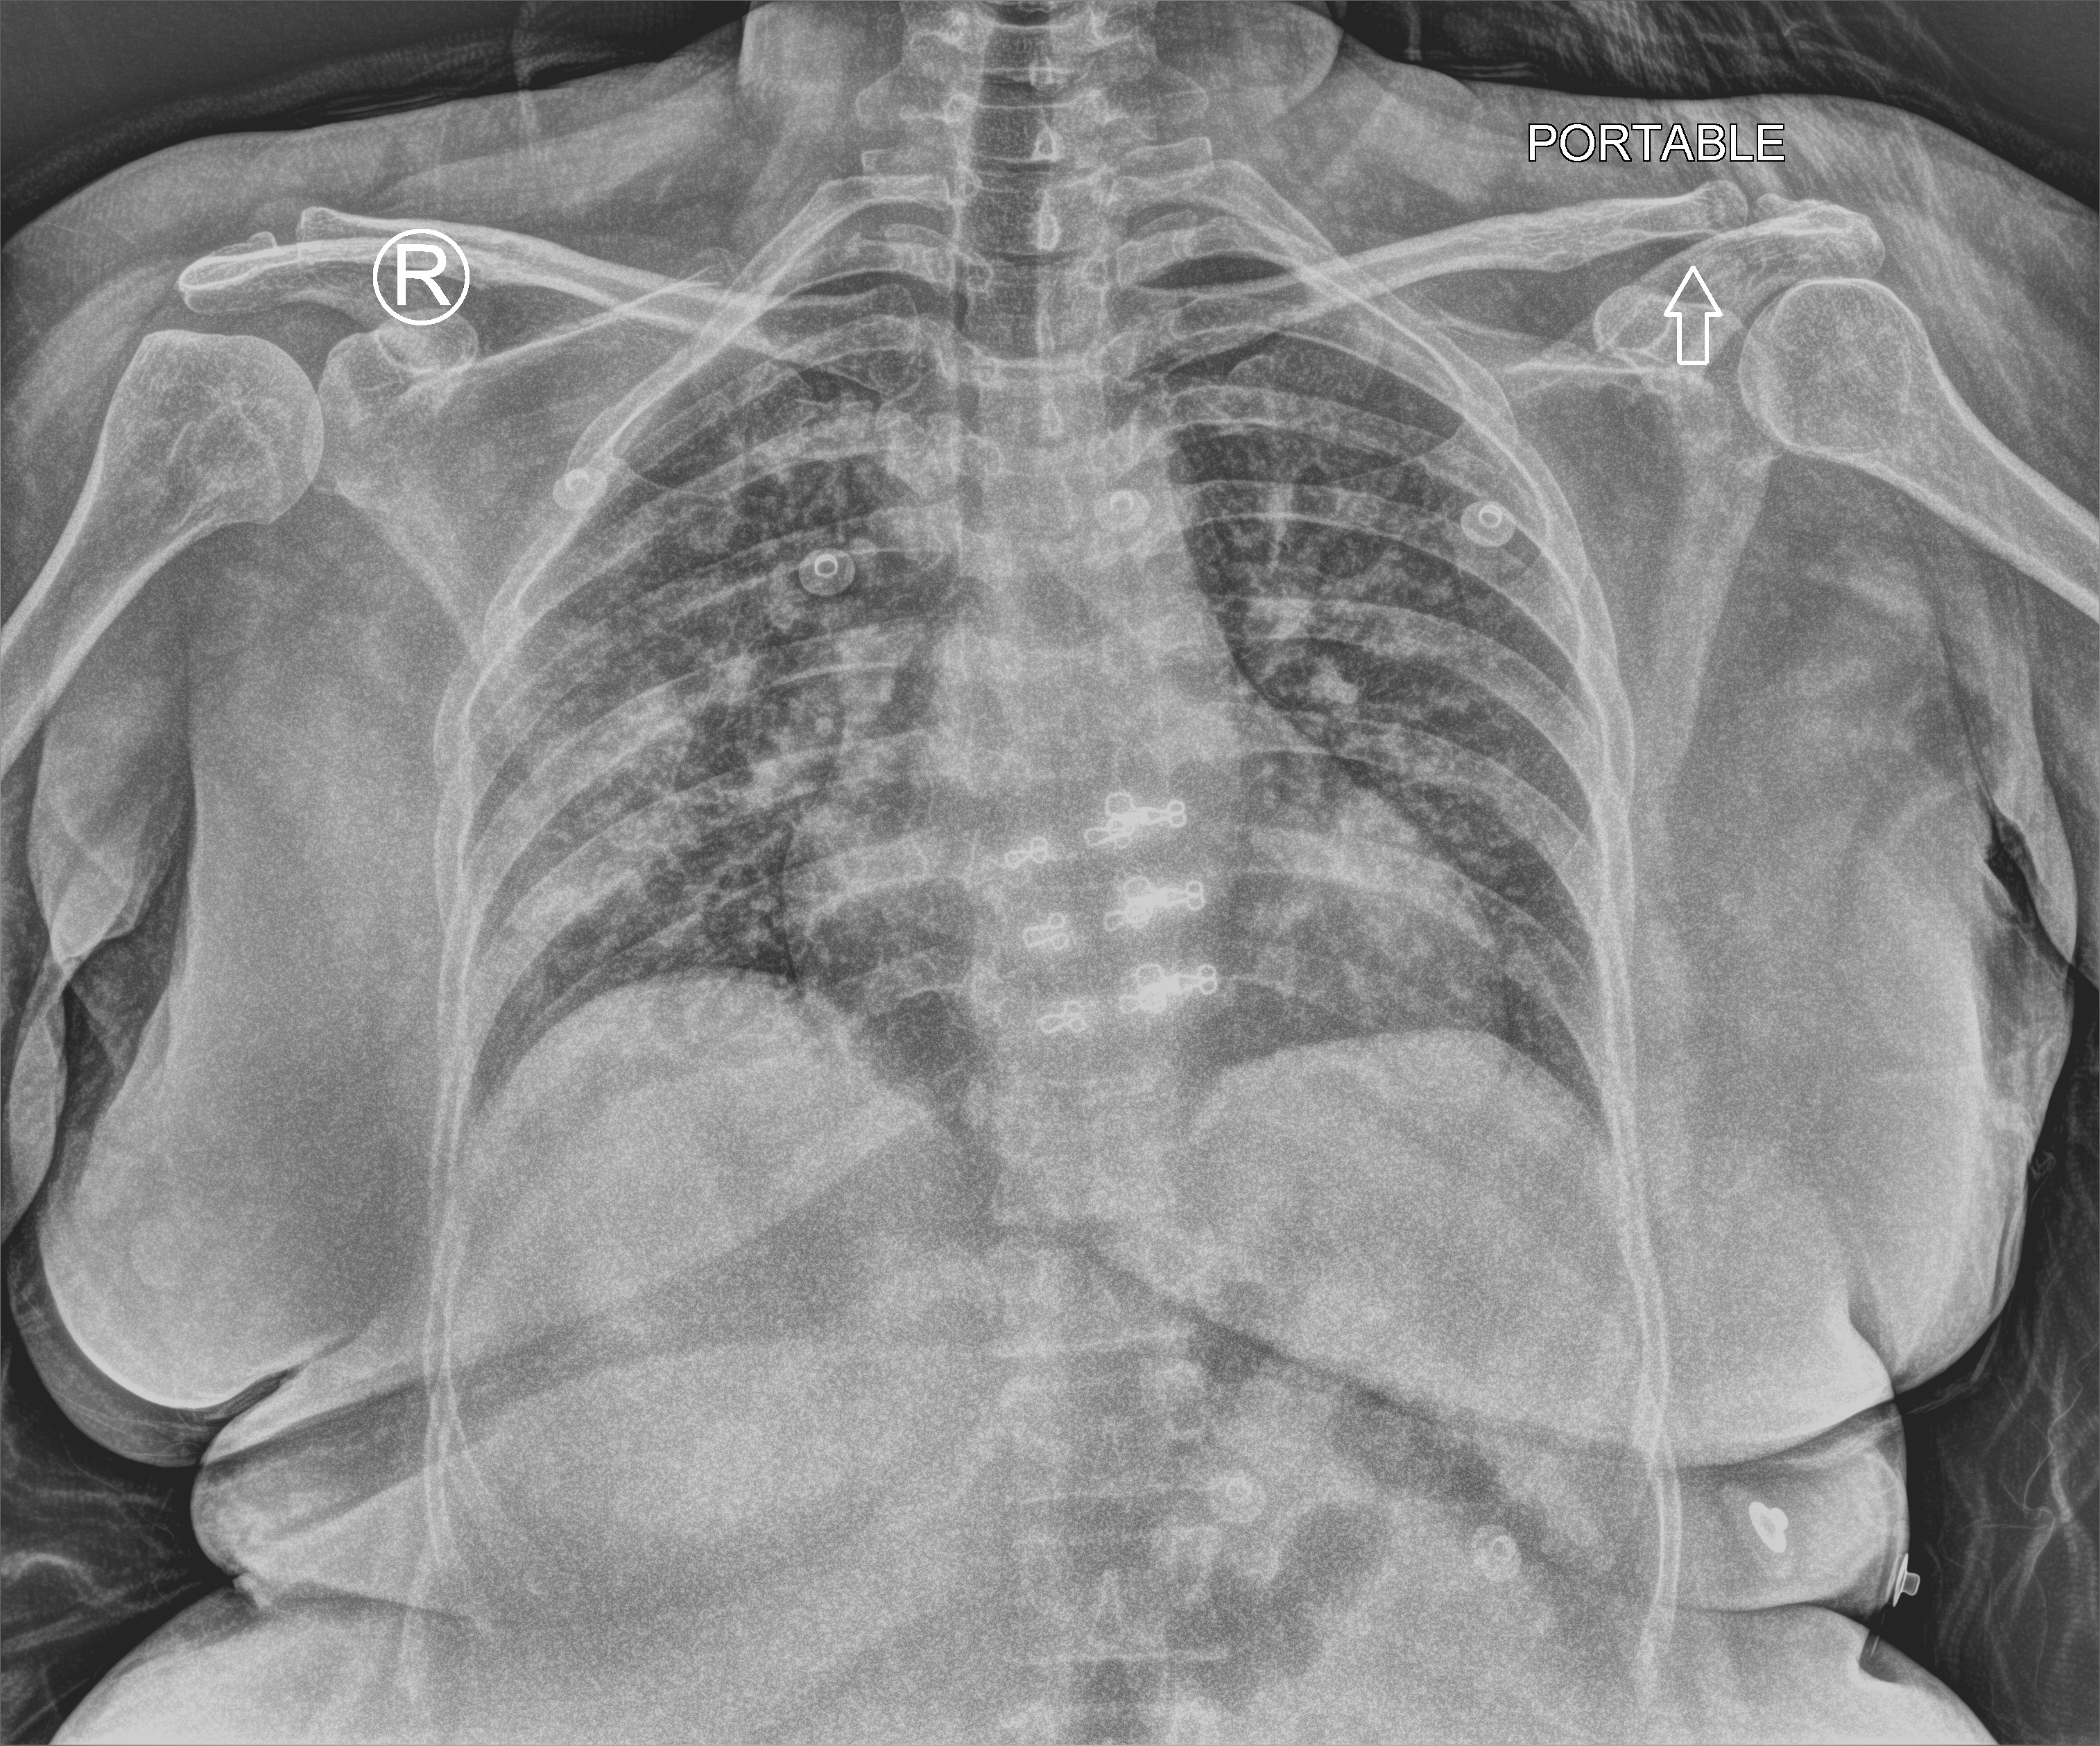
Bedside chest radiograph (computed radiography), anteroposterior (AP) projection. Female patient hospitalised with COVID-19, age 18–59 years.
Hospital-stay facts (about this admission, not read from this image; timing relative to this image not recorded):
- admitted to intensive care during this hospital stay: no
- smoking status (admission record): never